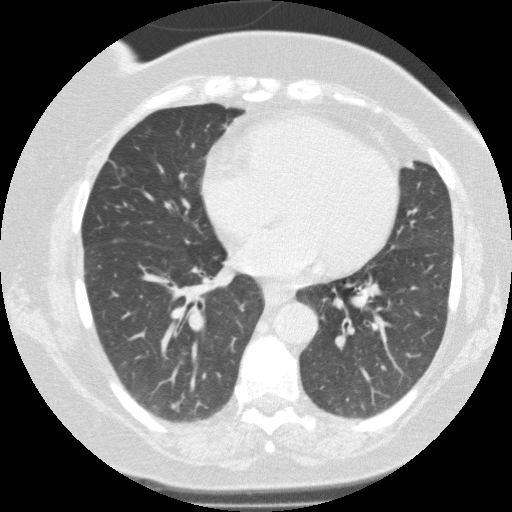
Low-dose screening chest CT, one axial slice; slice 62 of 146 in the series (ordered by position); reconstruction kernel FC01; 120 kVp; lung window (W 1500 / L -600 HU); 2 mm slice thickness; 512 × 512 image matrix.
Outlined on this slice (manually delineated by an expert):
- lesion 1 (nodule, lower lobe of right lung): box from (x=171, y=401) to (x=181, y=412) px